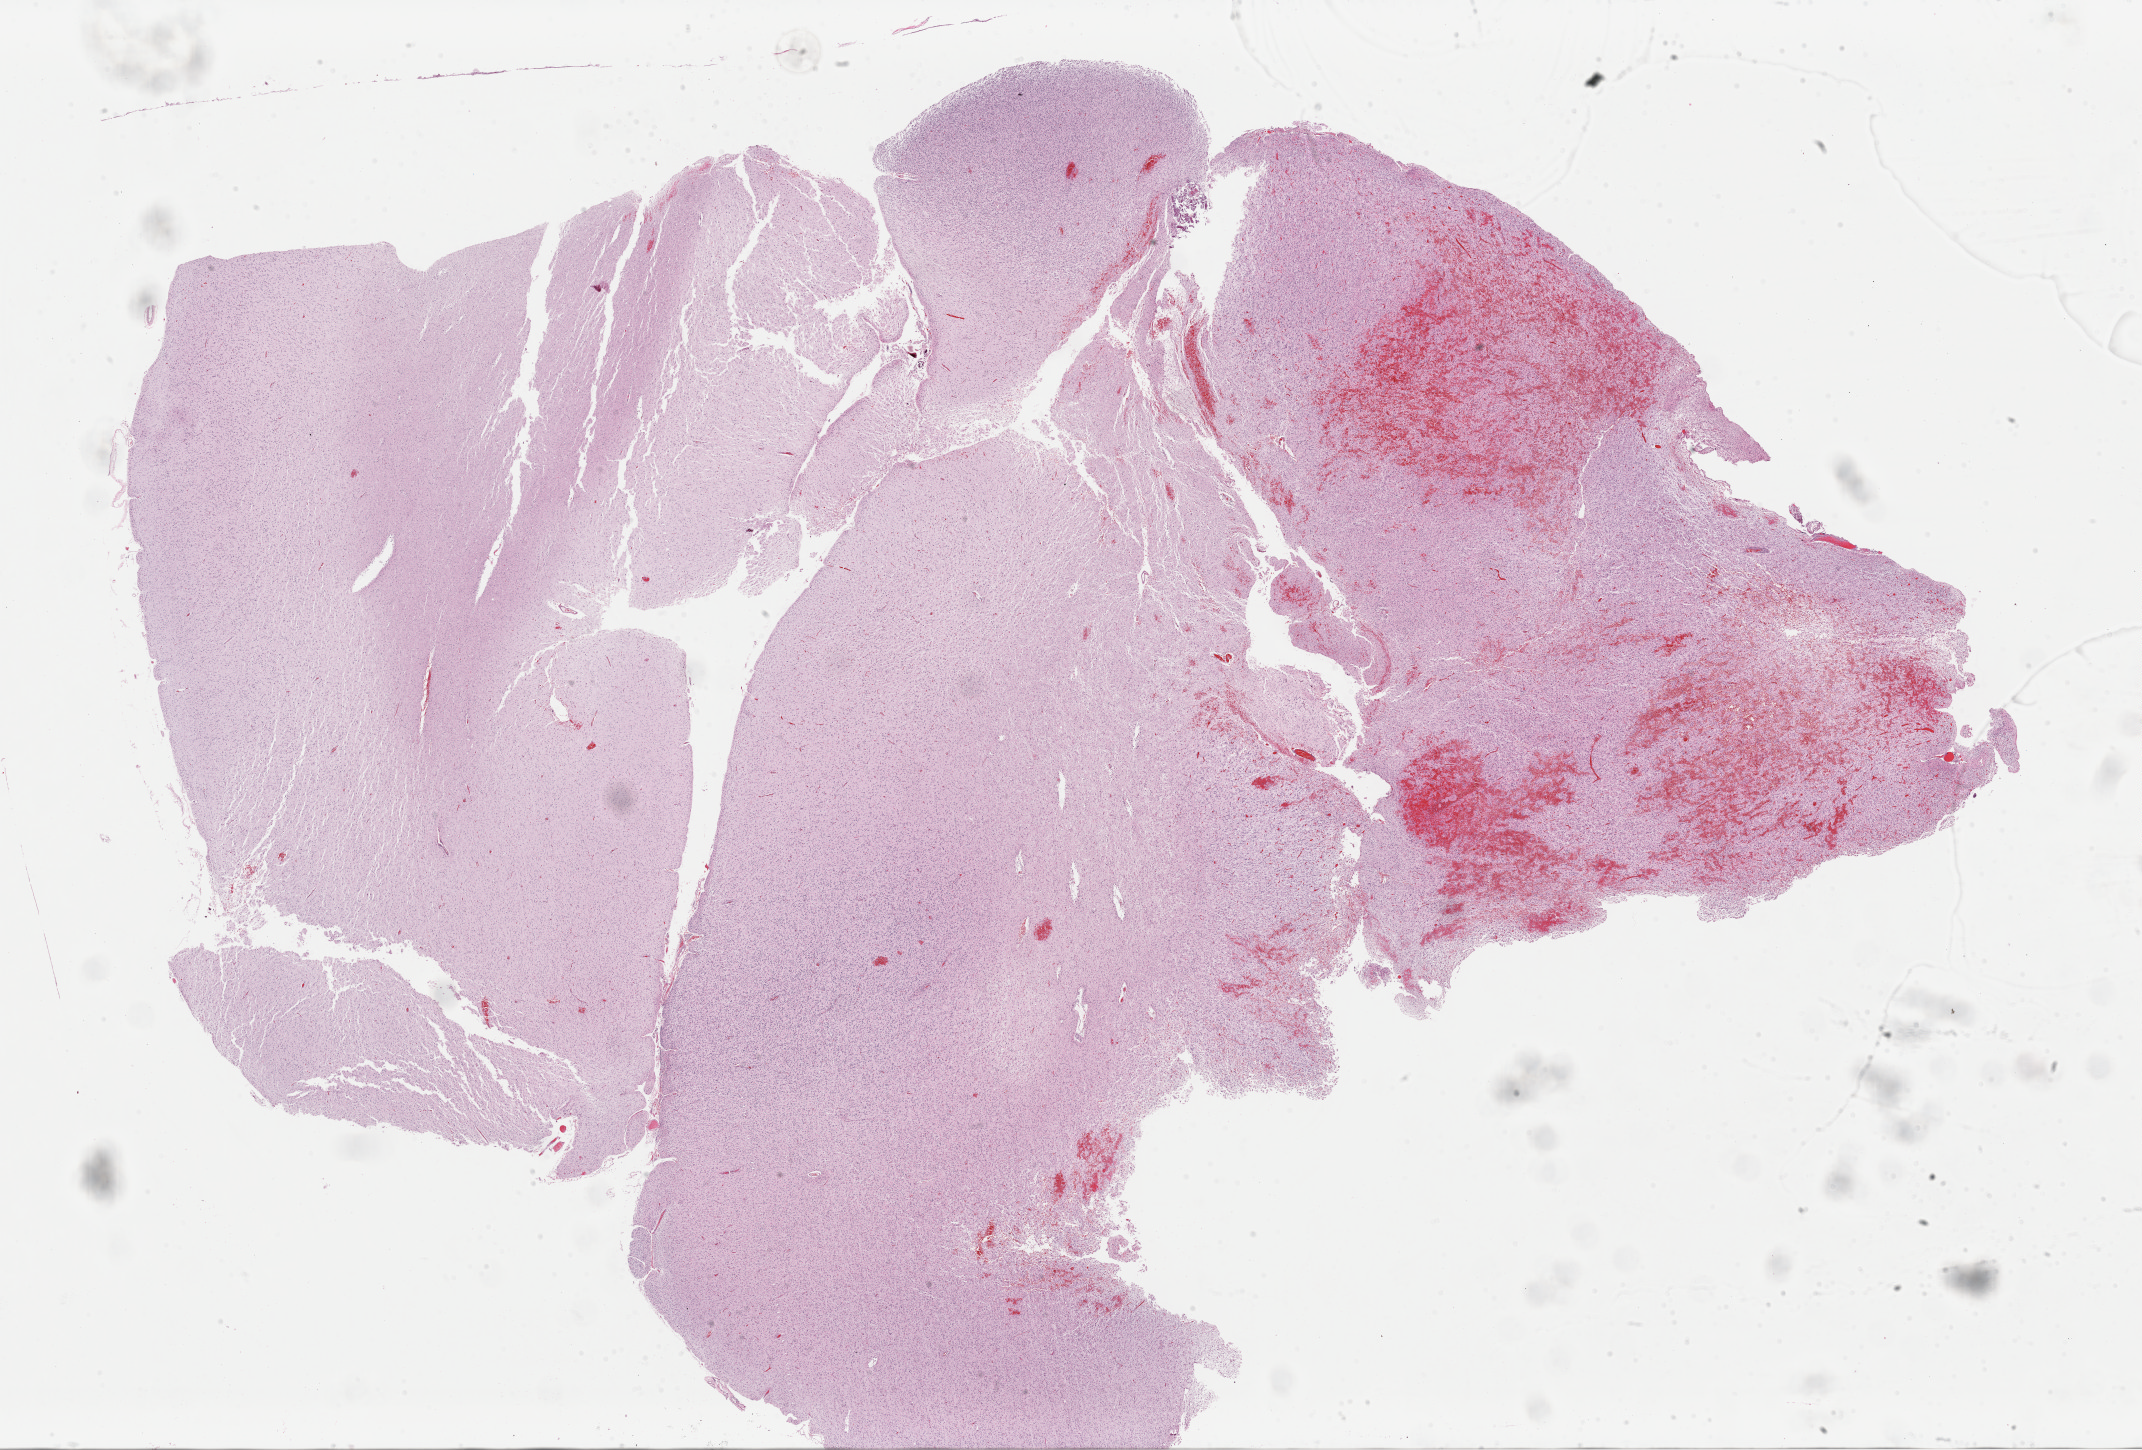
Whole-slide histology image, H&E, low-resolution overview of the scanned area, about 33.8 x 22.9 mm (slide scanned at 40x), formalin-fixed paraffin-embedded (FFPE) diagnostic section, primary tumour sample from the brain. Male patient; age at initial diagnosis 64 years. Histologic grade: G3 (poorly differentiated).
Histologic diagnosis: Astrocytoma, anaplastic (cerebrum).